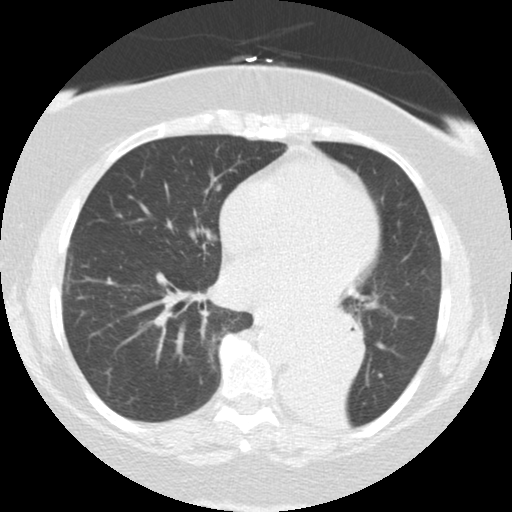
Low-dose screening chest CT, axial slice. Baseline annual screen. Lung window (W 1500 / L -600 HU). 512 × 512 image matrix, field of view 309 × 309 mm. Female, age 71 years at enrolment. Former smoker at enrolment.
Lesion marked by an expert reader, bounding box <282,304,367,383> (left, top, right, bottom; pixels). Screening reader's record for this exam (one nodule recorded; not confirmed to be the boxed lesion): non-calcified nodule or mass ≥4 mm, right middle lobe, 5 × 5 mm, smooth margins, soft tissue attenuation. Note: the box lies in the patient's left hemithorax on this image, whereas the reader's record names the right lung; they may be different findings. Official screen result: positive, change unspecified: nodule(s) >= 4 mm or enlarging nodule(s), mass(es), or other non-specific abnormalities suspicious for lung cancer. Participant outcome: lung cancer diagnosed 46 days after this screen — large cell carcinoma, NOS, left lower lobe, mediastinum, other location, poorly differentiated (G3), stage IV (AJCC 6th edition), 50 mm at pathology.